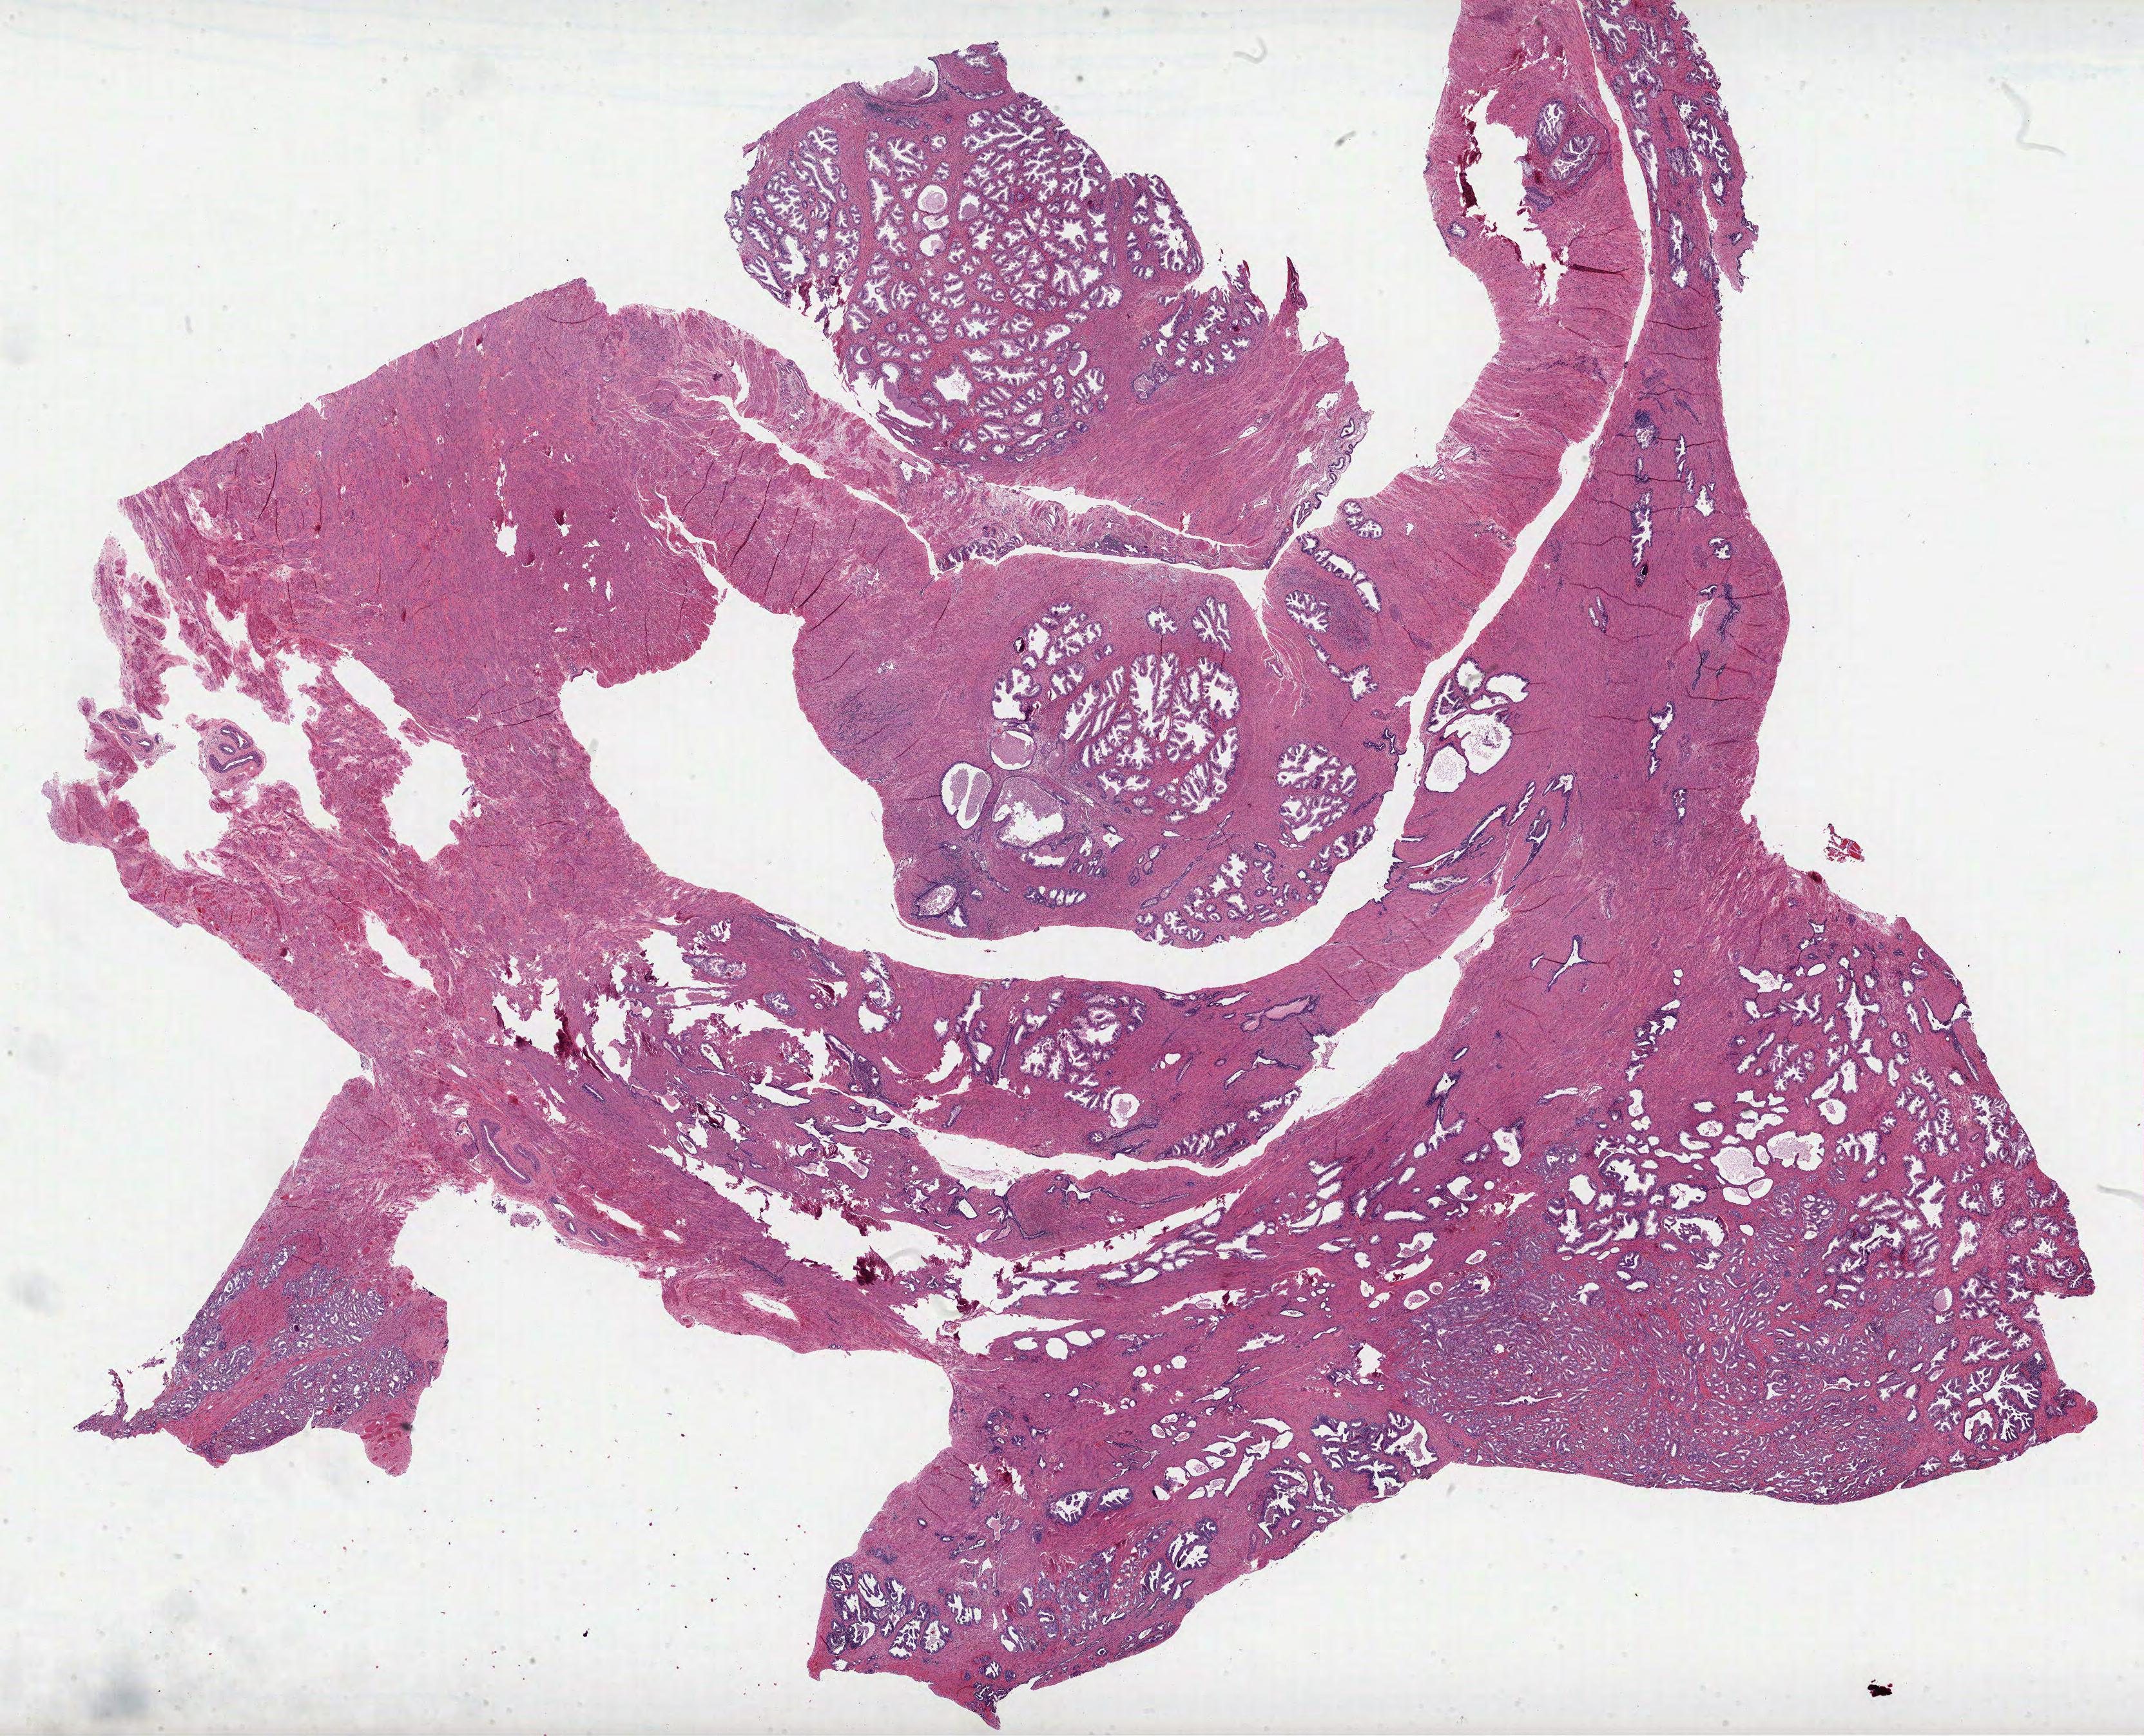
Digitized H&E-stained tissue section (whole slide), shown as a low-resolution overview of the whole scanned area (about 26.8 x 21.7 mm). FFPE section. Sample: primary tumour, prostate. Patient: male, age at initial diagnosis 71 years. Gleason score: 7 (3+4).
Pathologic diagnosis: Acinar cell carcinoma (prostate gland). Lymph nodes positive (case pathology): 0 of 40 examined.